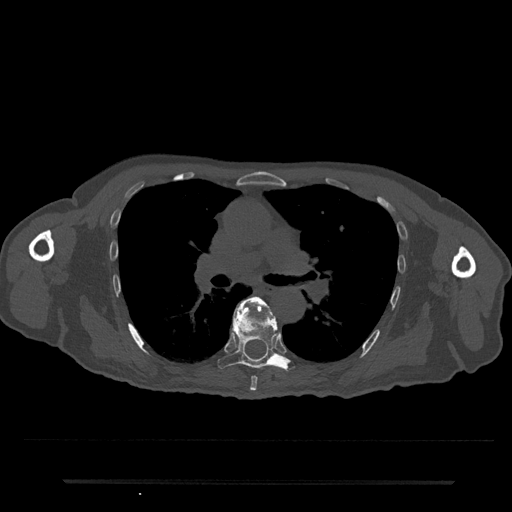
CT including the spine, one axial slice. Slice 494 of 797 in the series (ordered by position). Reconstruction kernel Br40s/3. Bone window (W 1800 / L 400 HU). 512 × 512 image matrix, field of view 427 × 427 mm. Male patient, age 74 years. Case-level facts recorded for this patient, not image findings: primary cancer: prostate.
Structures marked on this image (semi-automatic segmentation, software-assisted and operator-edited):
- T6 vertebra: bounding box <236,296,276,391> (left, top, right, bottom; pixels)
- T7 vertebra: <217,302,295,371>